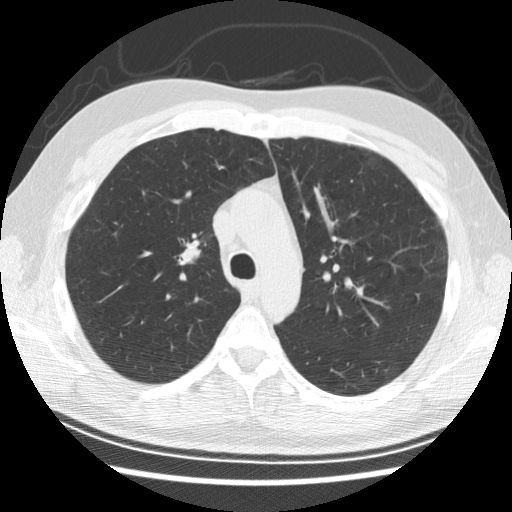
Axial slice from a low-dose chest CT screening exam, first (baseline) screen, lung window (W 1500 / L -600 HU), 2.5 mm slice thickness, slice 86 of 278 in the series, 512 × 512 image matrix. Male participant, aged 57 years at enrolment.
Lesion marked by an expert reader, bounding box [x1, y1, x2, y2] px = [163, 221, 221, 280]. The screening reader recorded 6 non-calcified nodules or masses ≥4 mm on this exam (right middle lobe, right middle lobe, right lower lobe, right middle lobe, right middle lobe, right lower lobe); which of them this box marks is not recorded. Later outcome: lung cancer diagnosed 766 days after this screen (after the second annual screen) — adenocarcinoma, NOS, right upper lobe, poorly differentiated (G3), stage IB (AJCC 6th edition), 25 mm at pathology.